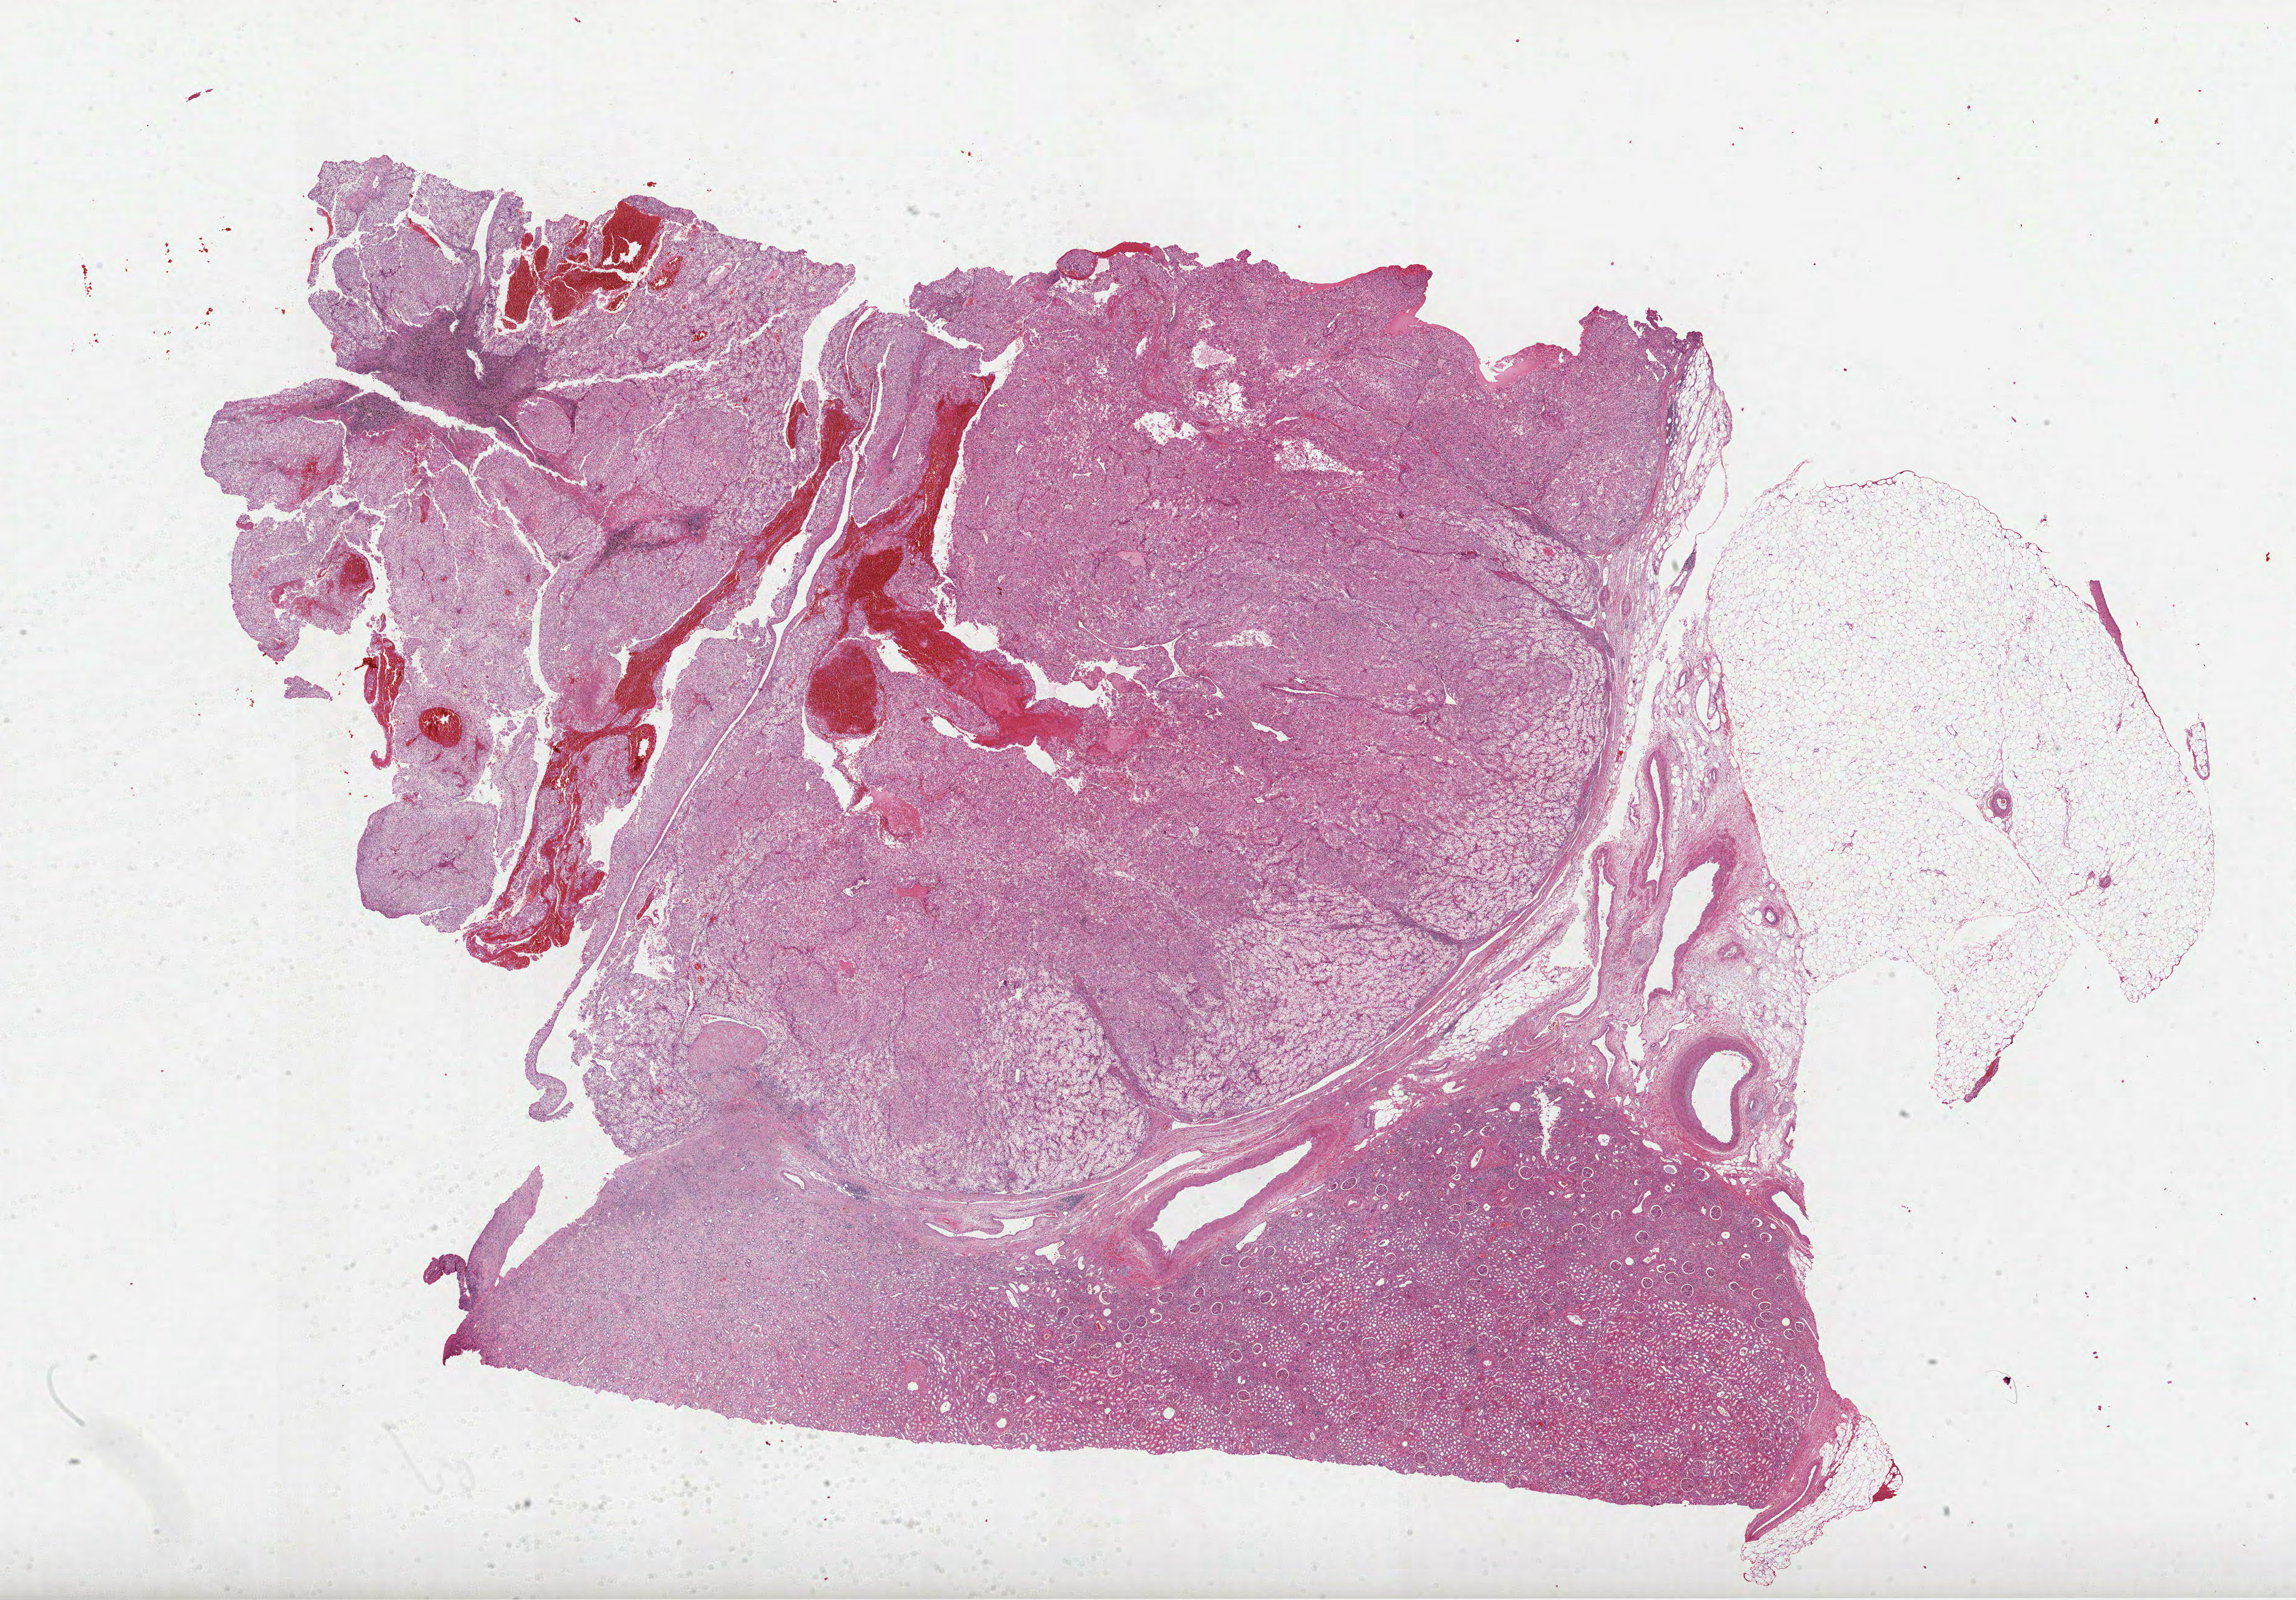
Whole-slide histology image, H&E-stained — shown as a low-resolution overview of the whole scanned area (about 30.2 x 21.1 mm), FFPE section, kidney, primary tumour sample. Male, age 61 years at initial diagnosis. Histologic grade: G3 (poorly differentiated).
AJCC pathologic stage: IV. Laterality: right. TNM: T3b NX M1. Histologic diagnosis: Clear cell adenocarcinoma, NOS.